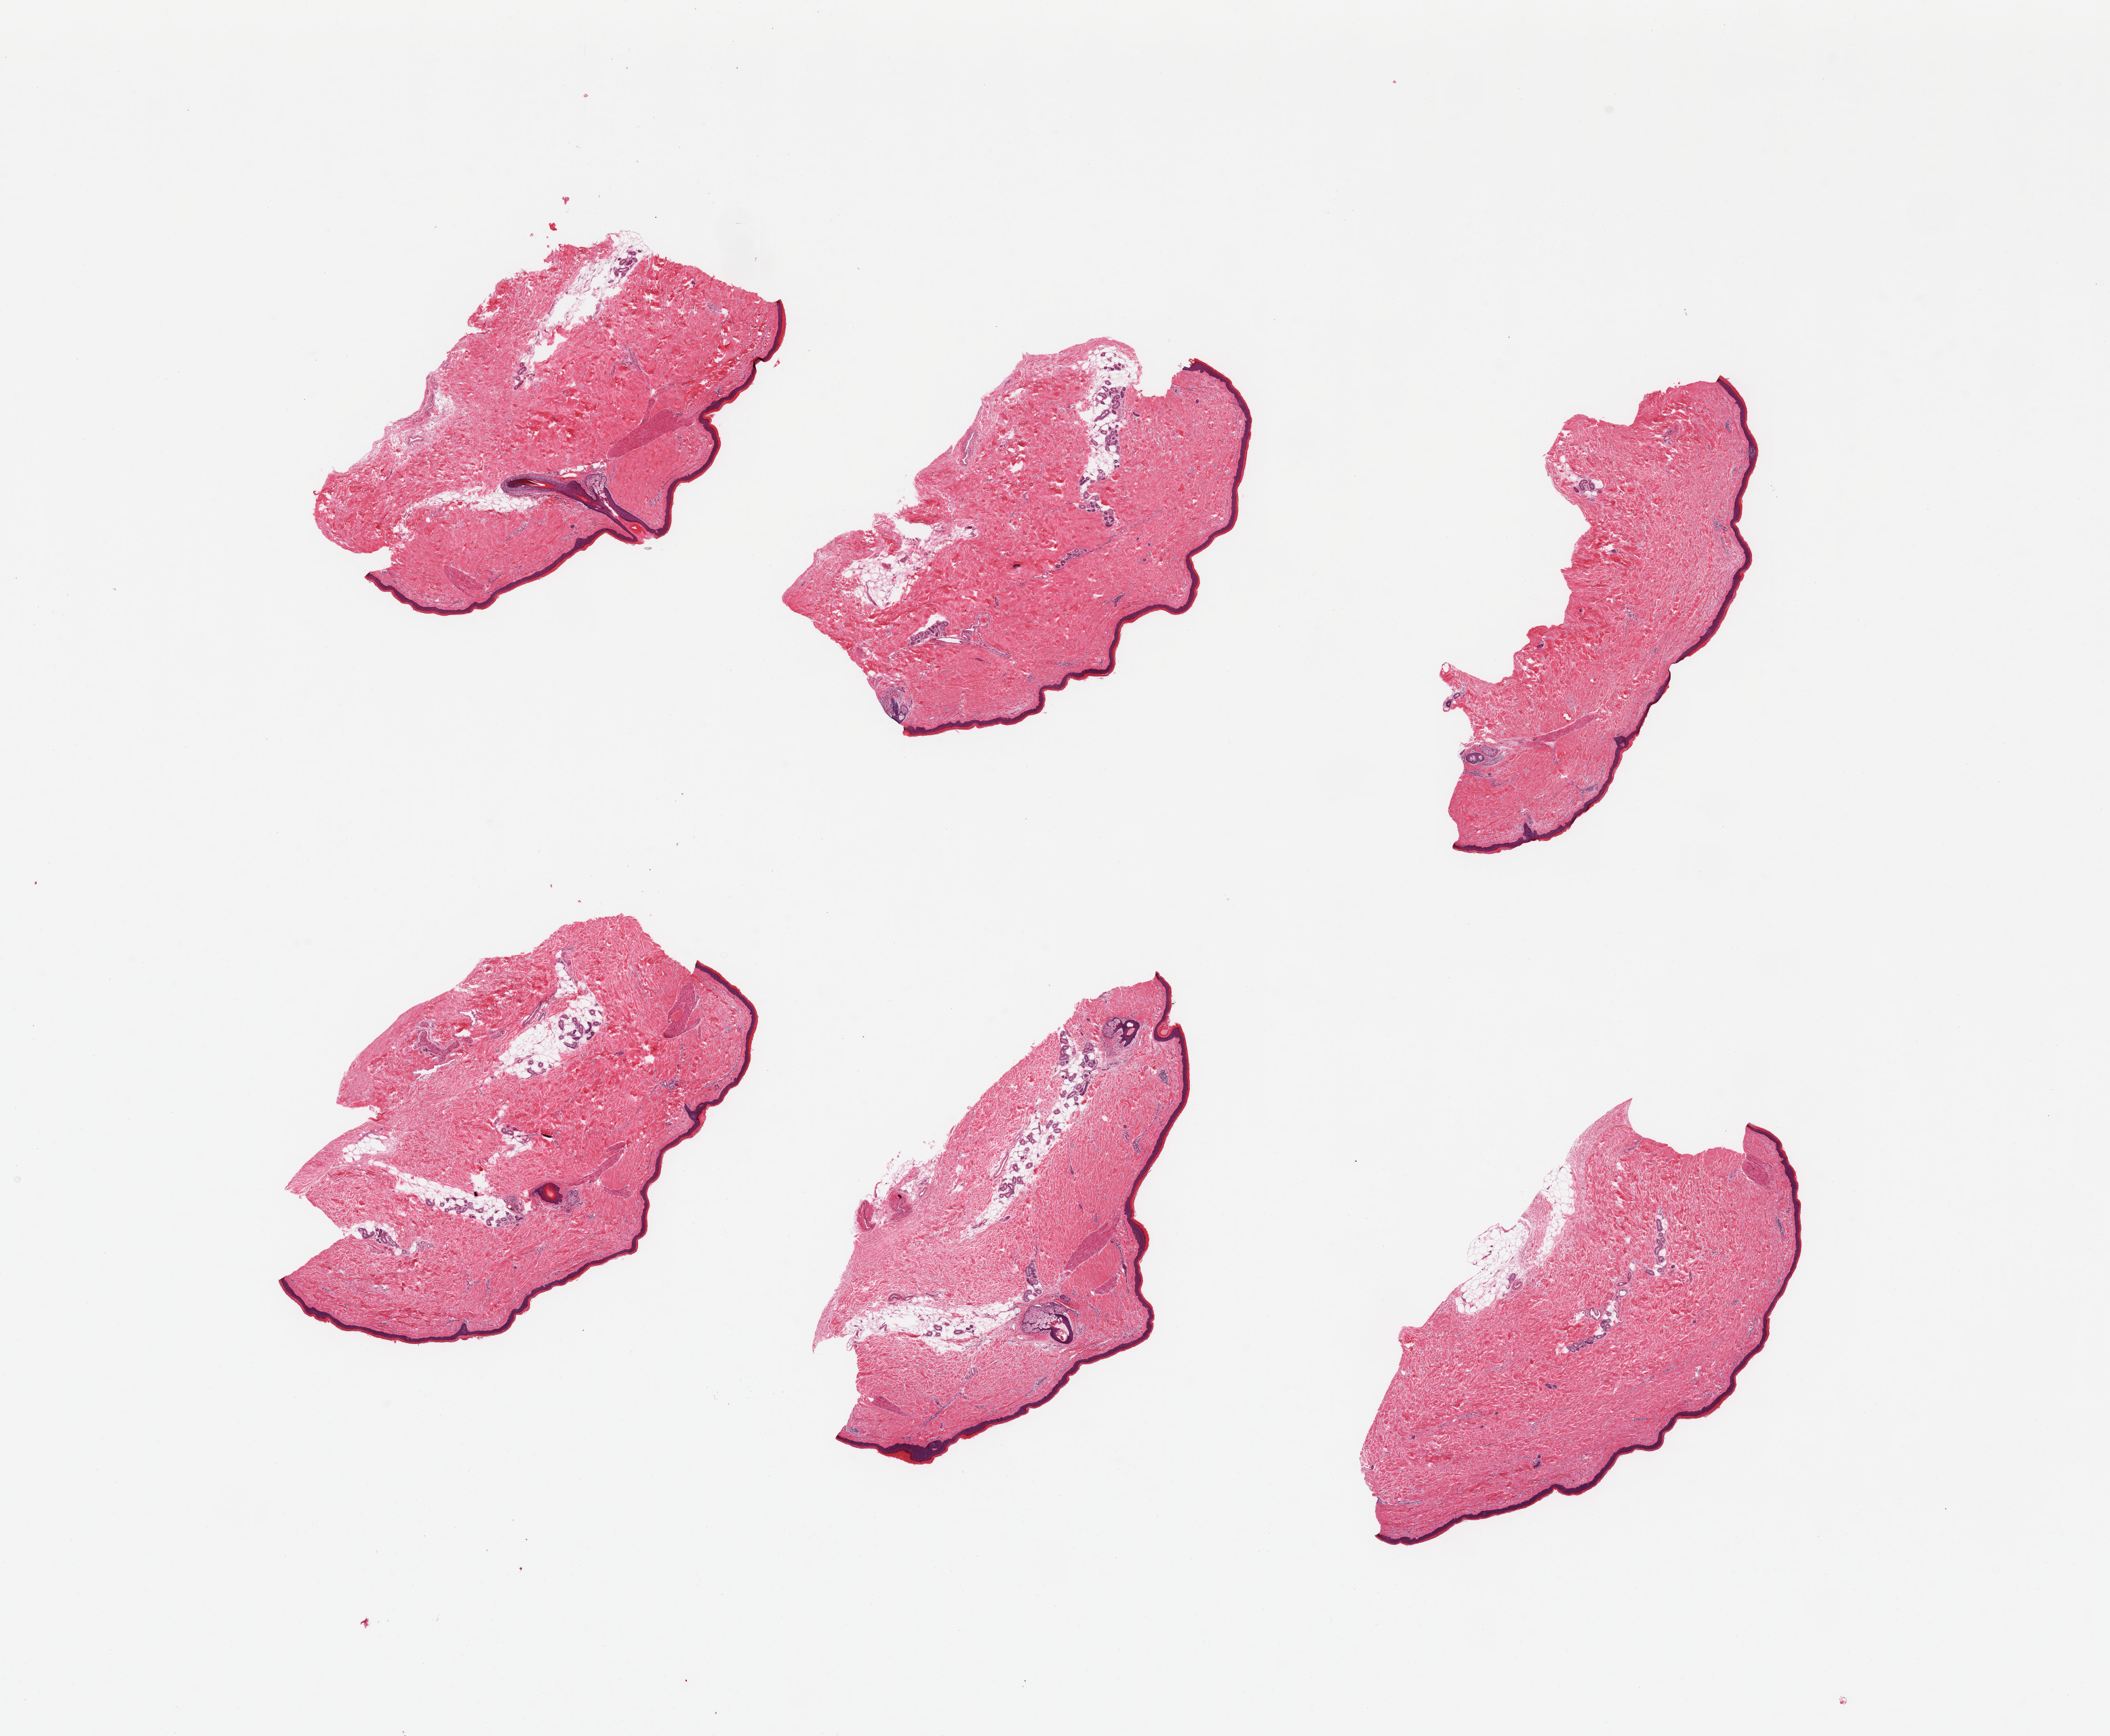
Digitized haematoxylin and eosin-stained section, low-resolution overview of the scanned area, about 24.6 x 20.2 mm (slide scanned at 20x), PAXgene-fixed paraffin-embedded (PFPE) section, target tissue: skin of lower leg, donor tissue sample. Donor sex: male.
Reviewer comment on this tissue sample: 6 pieces; well trimmed; dermal fat 10%; several hair follicles.